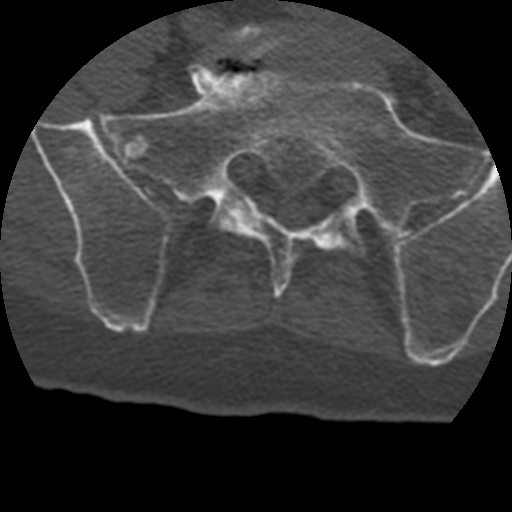
CT including the spine, one axial slice. Position 24 of 399 along the scan axis. Reconstruction kernel STANDARD. Bone window (W 1800 / L 400 HU). 512 × 512 image matrix, field of view 160 × 160 mm. Patient age 69 years. Case-level facts recorded for this patient, not image findings: primary cancer: prostate.
Structures marked on this image (semi-automatically segmented with operator editing):
- L5 vertebra: bounding box (x1, y1, x2, y2) in pixels: (215, 24, 291, 60)